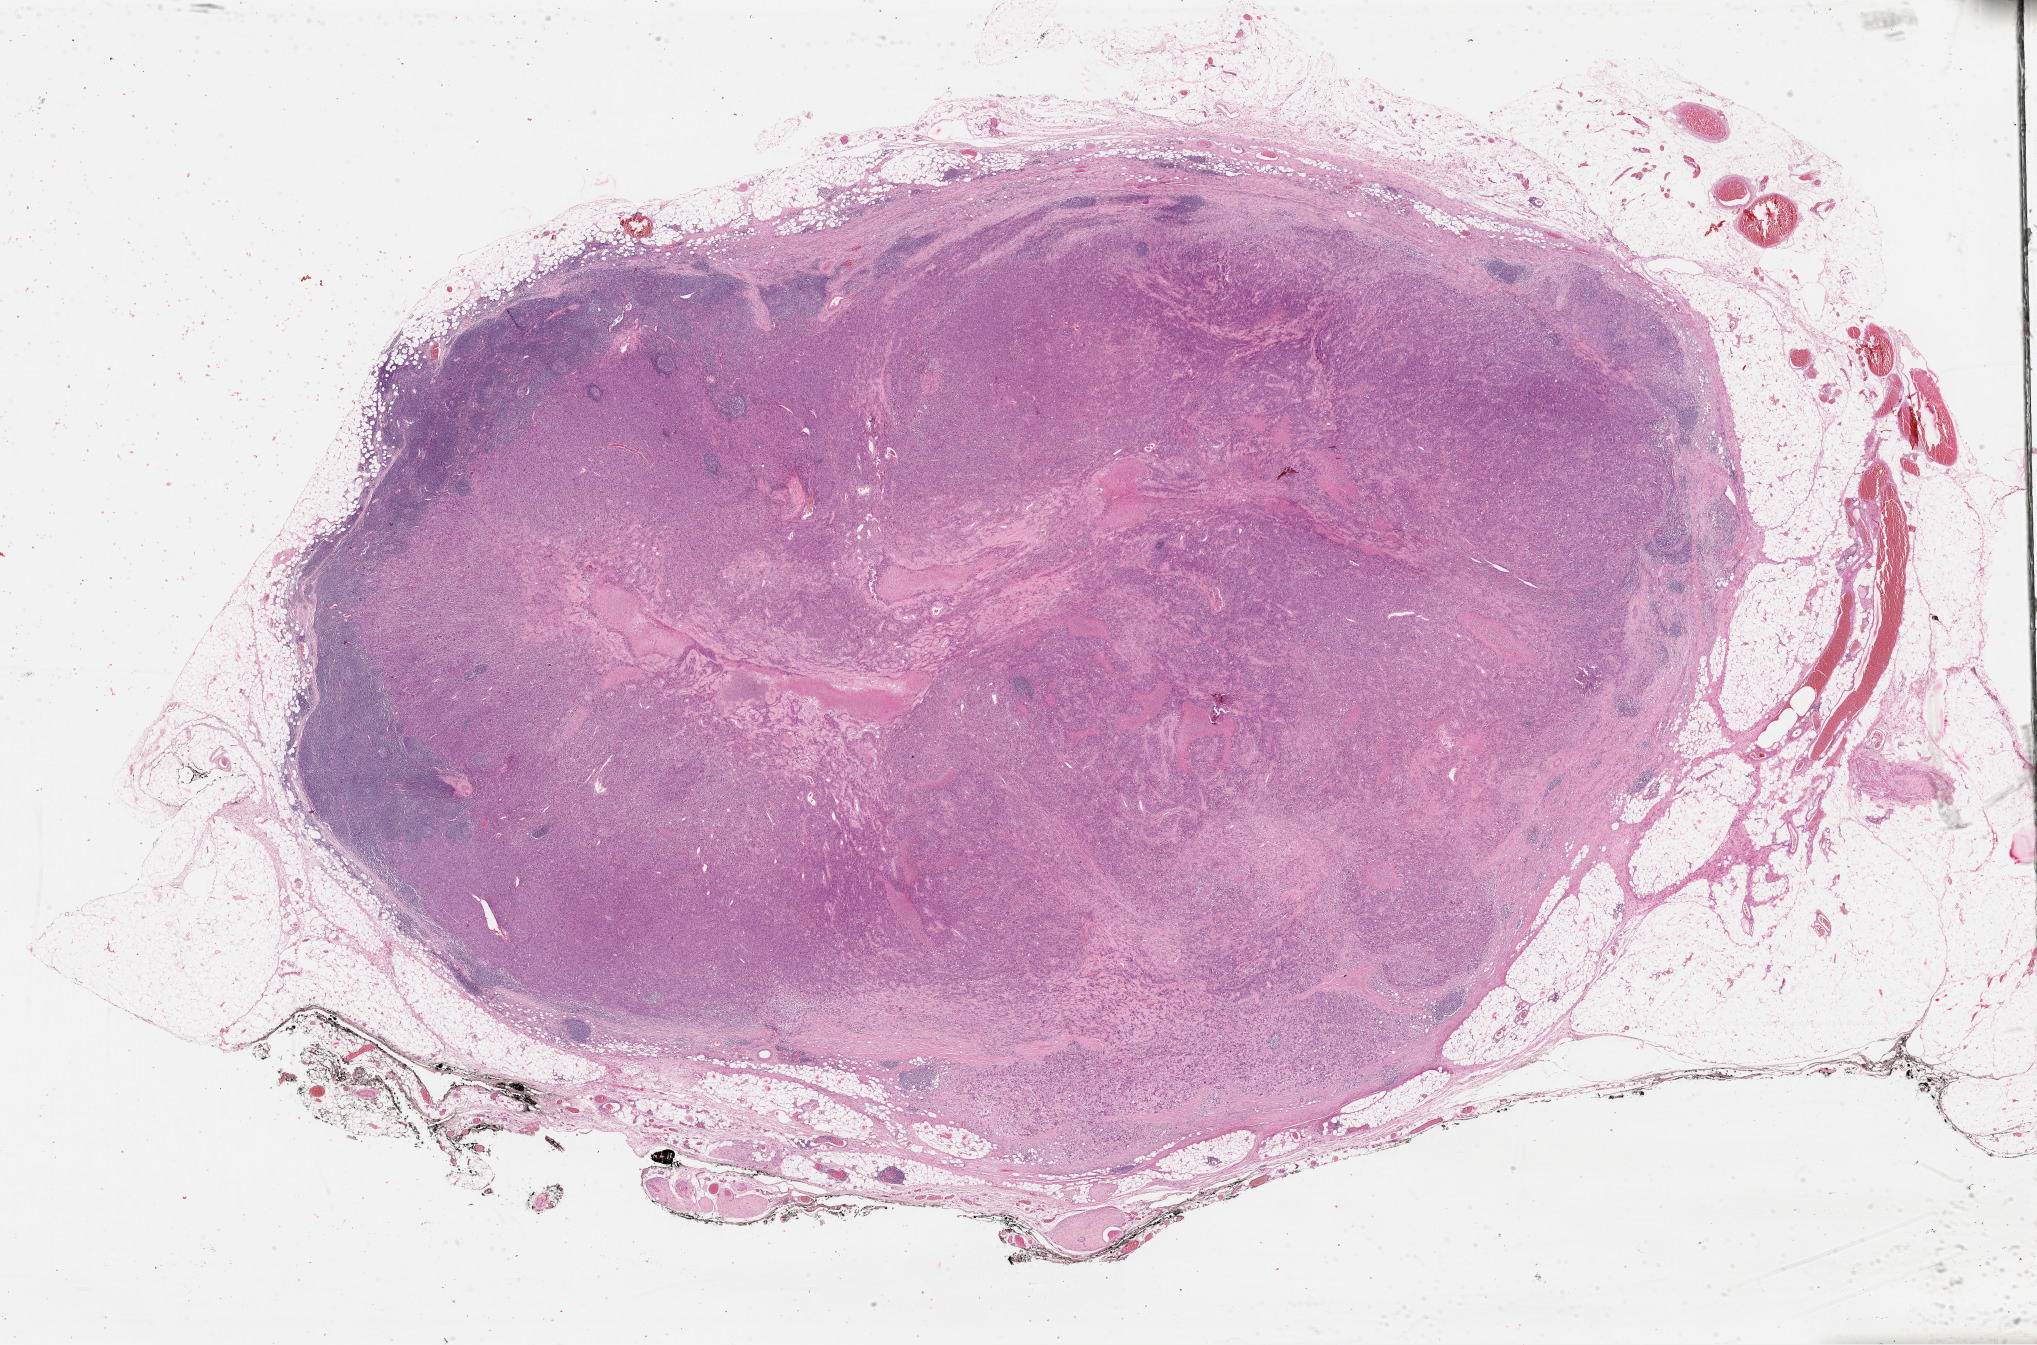
Digitized H&E-stained tissue section (whole slide), a low-resolution overview of the entire scanned area, about 32.0 x 21.2 mm (slide scanned at 40x). FFPE section. Primary tumour sample from the skin. Patient: male, age at initial diagnosis 71 years.
Histologic diagnosis: Malignant melanoma, NOS.